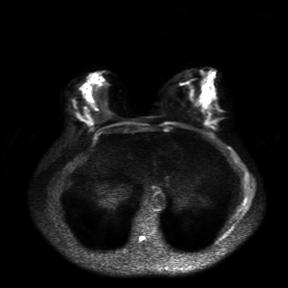
Breast MRI, one axial slice. Position 10 of 30 along the scan axis. Diffusion-weighted series; image 2 of 4 stored at this slice position (different b-values; order by instance number). 3 T. 4 mm slice thickness. 288 × 288 image matrix, field of view 360 × 360 mm. Female patient.
Structures marked on this image (expert manual segmentation):
- tumour on diffusion-weighted imaging: bounding box (x1, y1, x2, y2) in pixels: (205, 100, 217, 118)